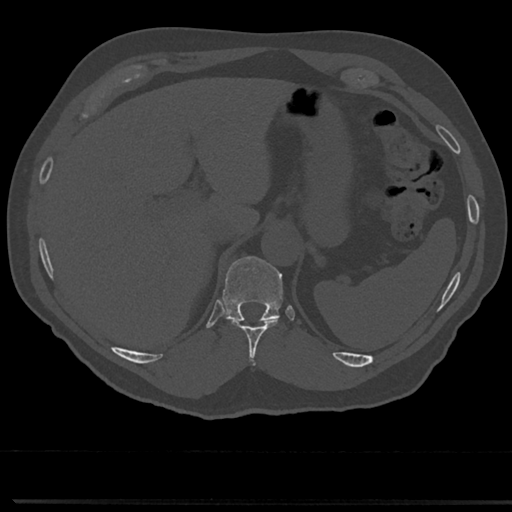
CT including the spine, one axial slice. Reconstruction kernel Br40s/3. 120 kVp. Bone window (W 1800 / L 400 HU). 512 × 512 image matrix, field of view 355 × 355 mm. Patient: male, 61 years. Case-level facts recorded for this patient, not image findings: primary cancer: prostate.
Structures marked on this image (semi-automatic segmentation, software-assisted and operator-edited):
- T10 vertebra: bounding box (x1, y1, x2, y2) in pixels: (228, 318, 280, 356)
- T11 vertebra: (223, 256, 283, 322)